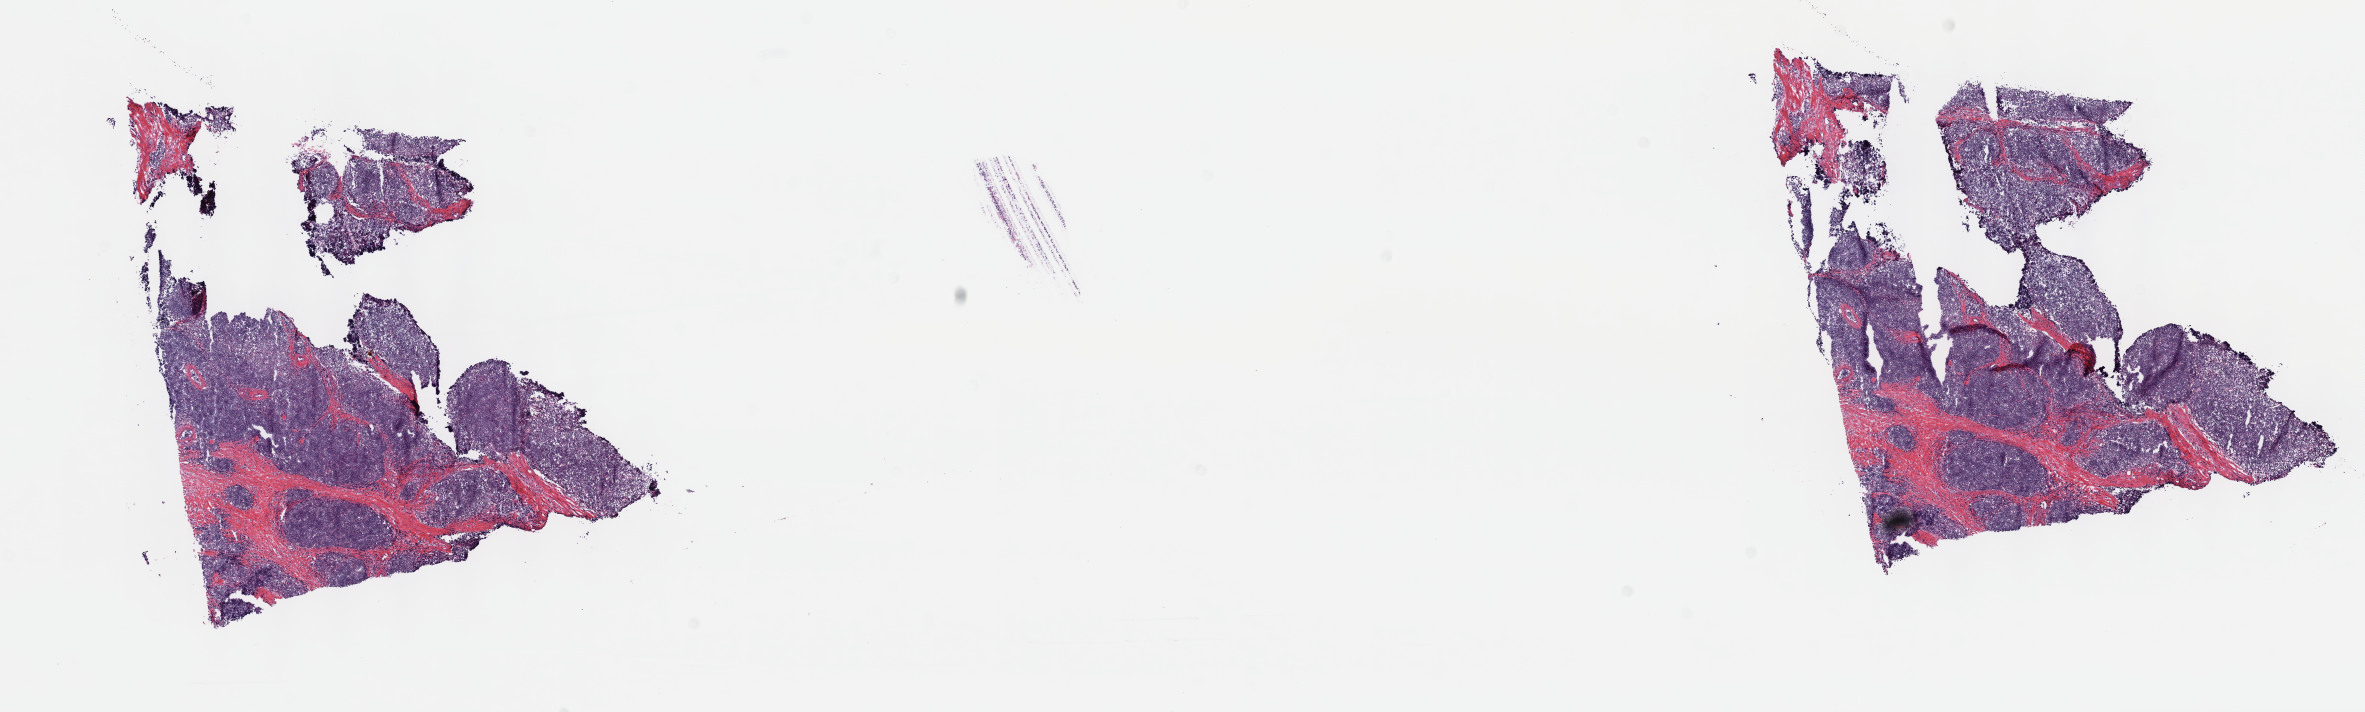
H&E-stained whole-slide image — a low-resolution overview of the entire scanned area, about 19.1 x 5.8 mm (slide scanned at 40x); frozen section from the top of the tissue portion; sample: primary tumour, thymus. Patient: female, age at initial diagnosis 57 years. Pathologist review of this section (percent, as recorded): tumour cells 100%, tumour nuclei 70%, normal cells 0%, stromal cells 0%, necrosis 0%. Infiltration values recorded for this section: lymphocyte infiltration 2%, monocyte infiltration 0%, neutrophil infiltration 0%.
Diagnosis: Thymoma, type B1, NOS.